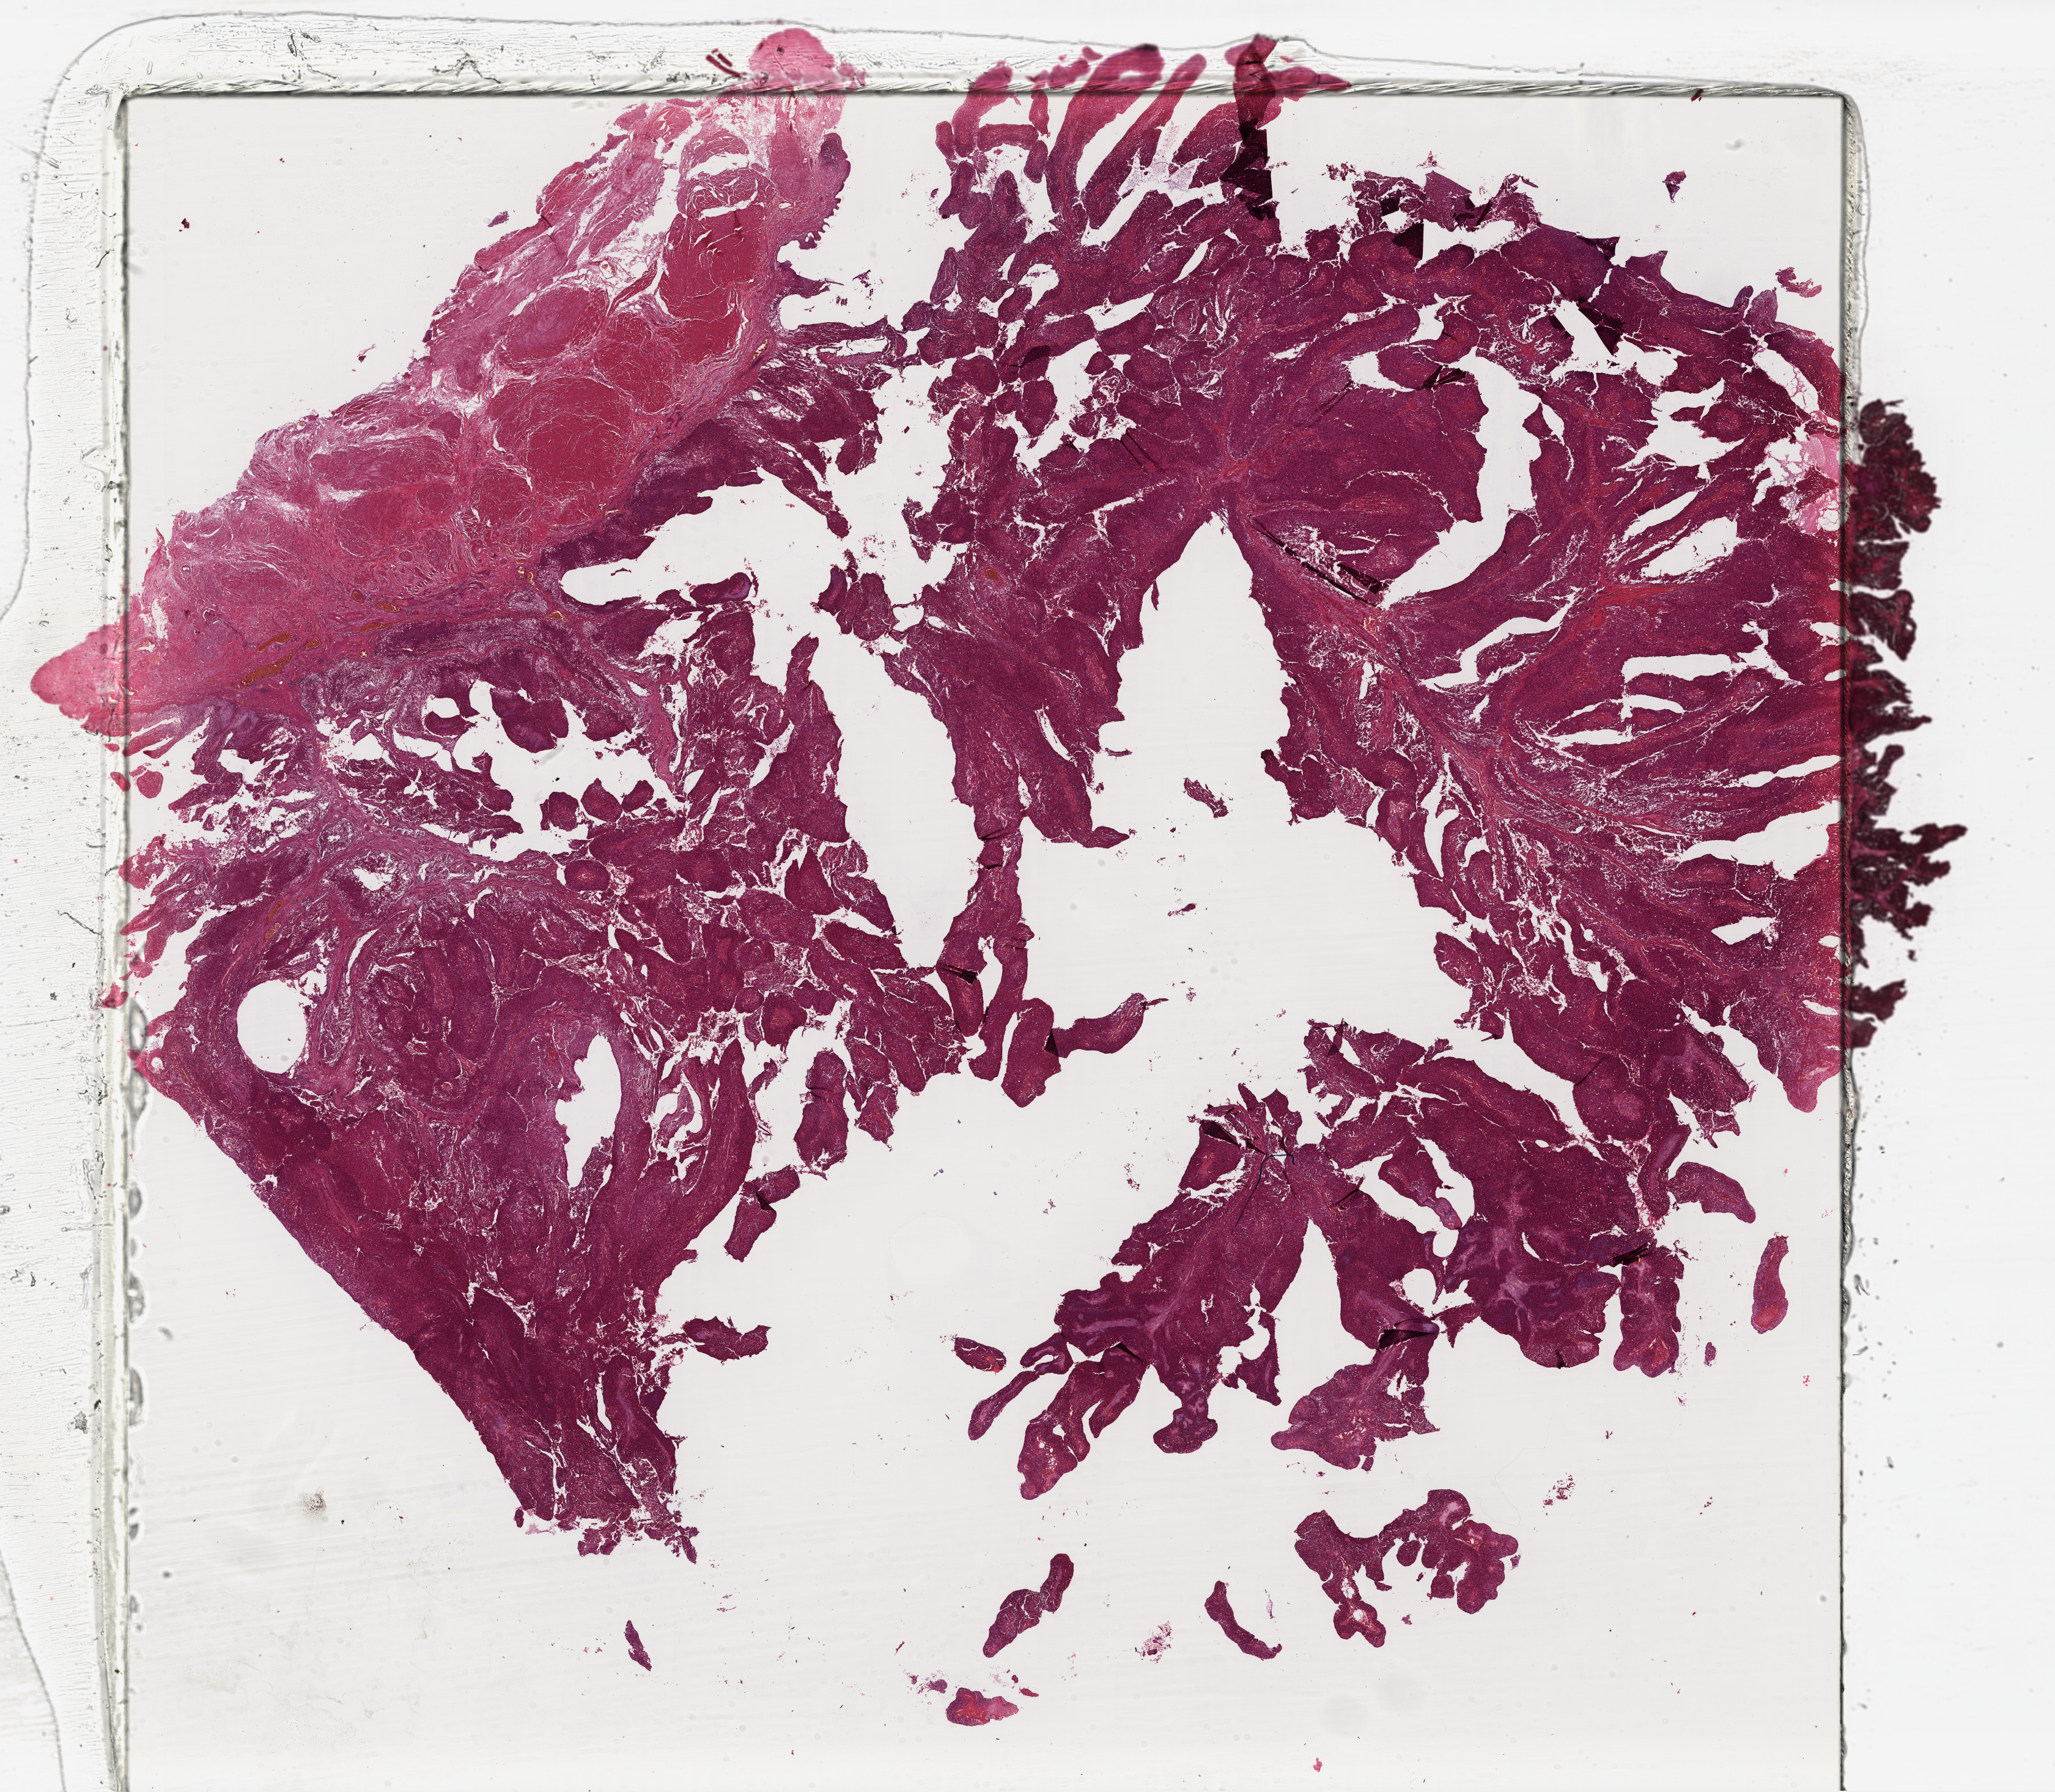
Hematoxylin and eosin (H&E) stained whole-slide image — low-resolution overview of the scanned area, about 26.4 x 23.0 mm; formalin-fixed paraffin-embedded (FFPE) diagnostic section; bladder, primary tumour sample. Patient: male, age at initial diagnosis 62 years. Histologic grade: low grade.
• diagnosis: Papillary transitional cell carcinoma
• TNM: T2 N0 M0
• AJCC pathologic stage: II